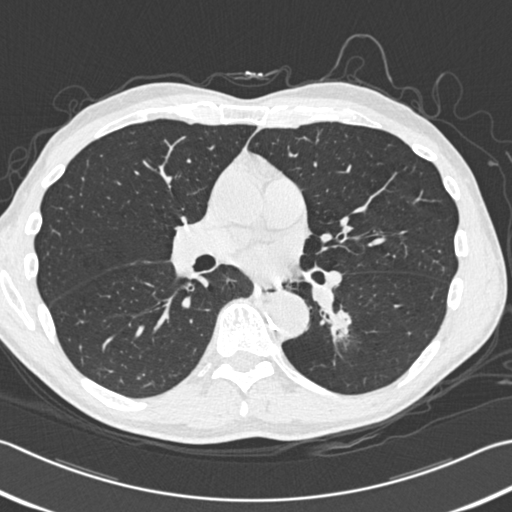
Low-dose screening chest CT, one axial slice. Slice 189 of 354 in the series (ordered by position). Reconstruction kernel B30f. 120 kVp. Lung window (W 1500 / L -600 HU). 512 × 512 image matrix, field of view 346 × 346 mm.
Structures marked on this image (manually delineated by an expert):
- lesion 1 (tumor, lower lobe of left lung): box from (x=336, y=309) to (x=351, y=329) px